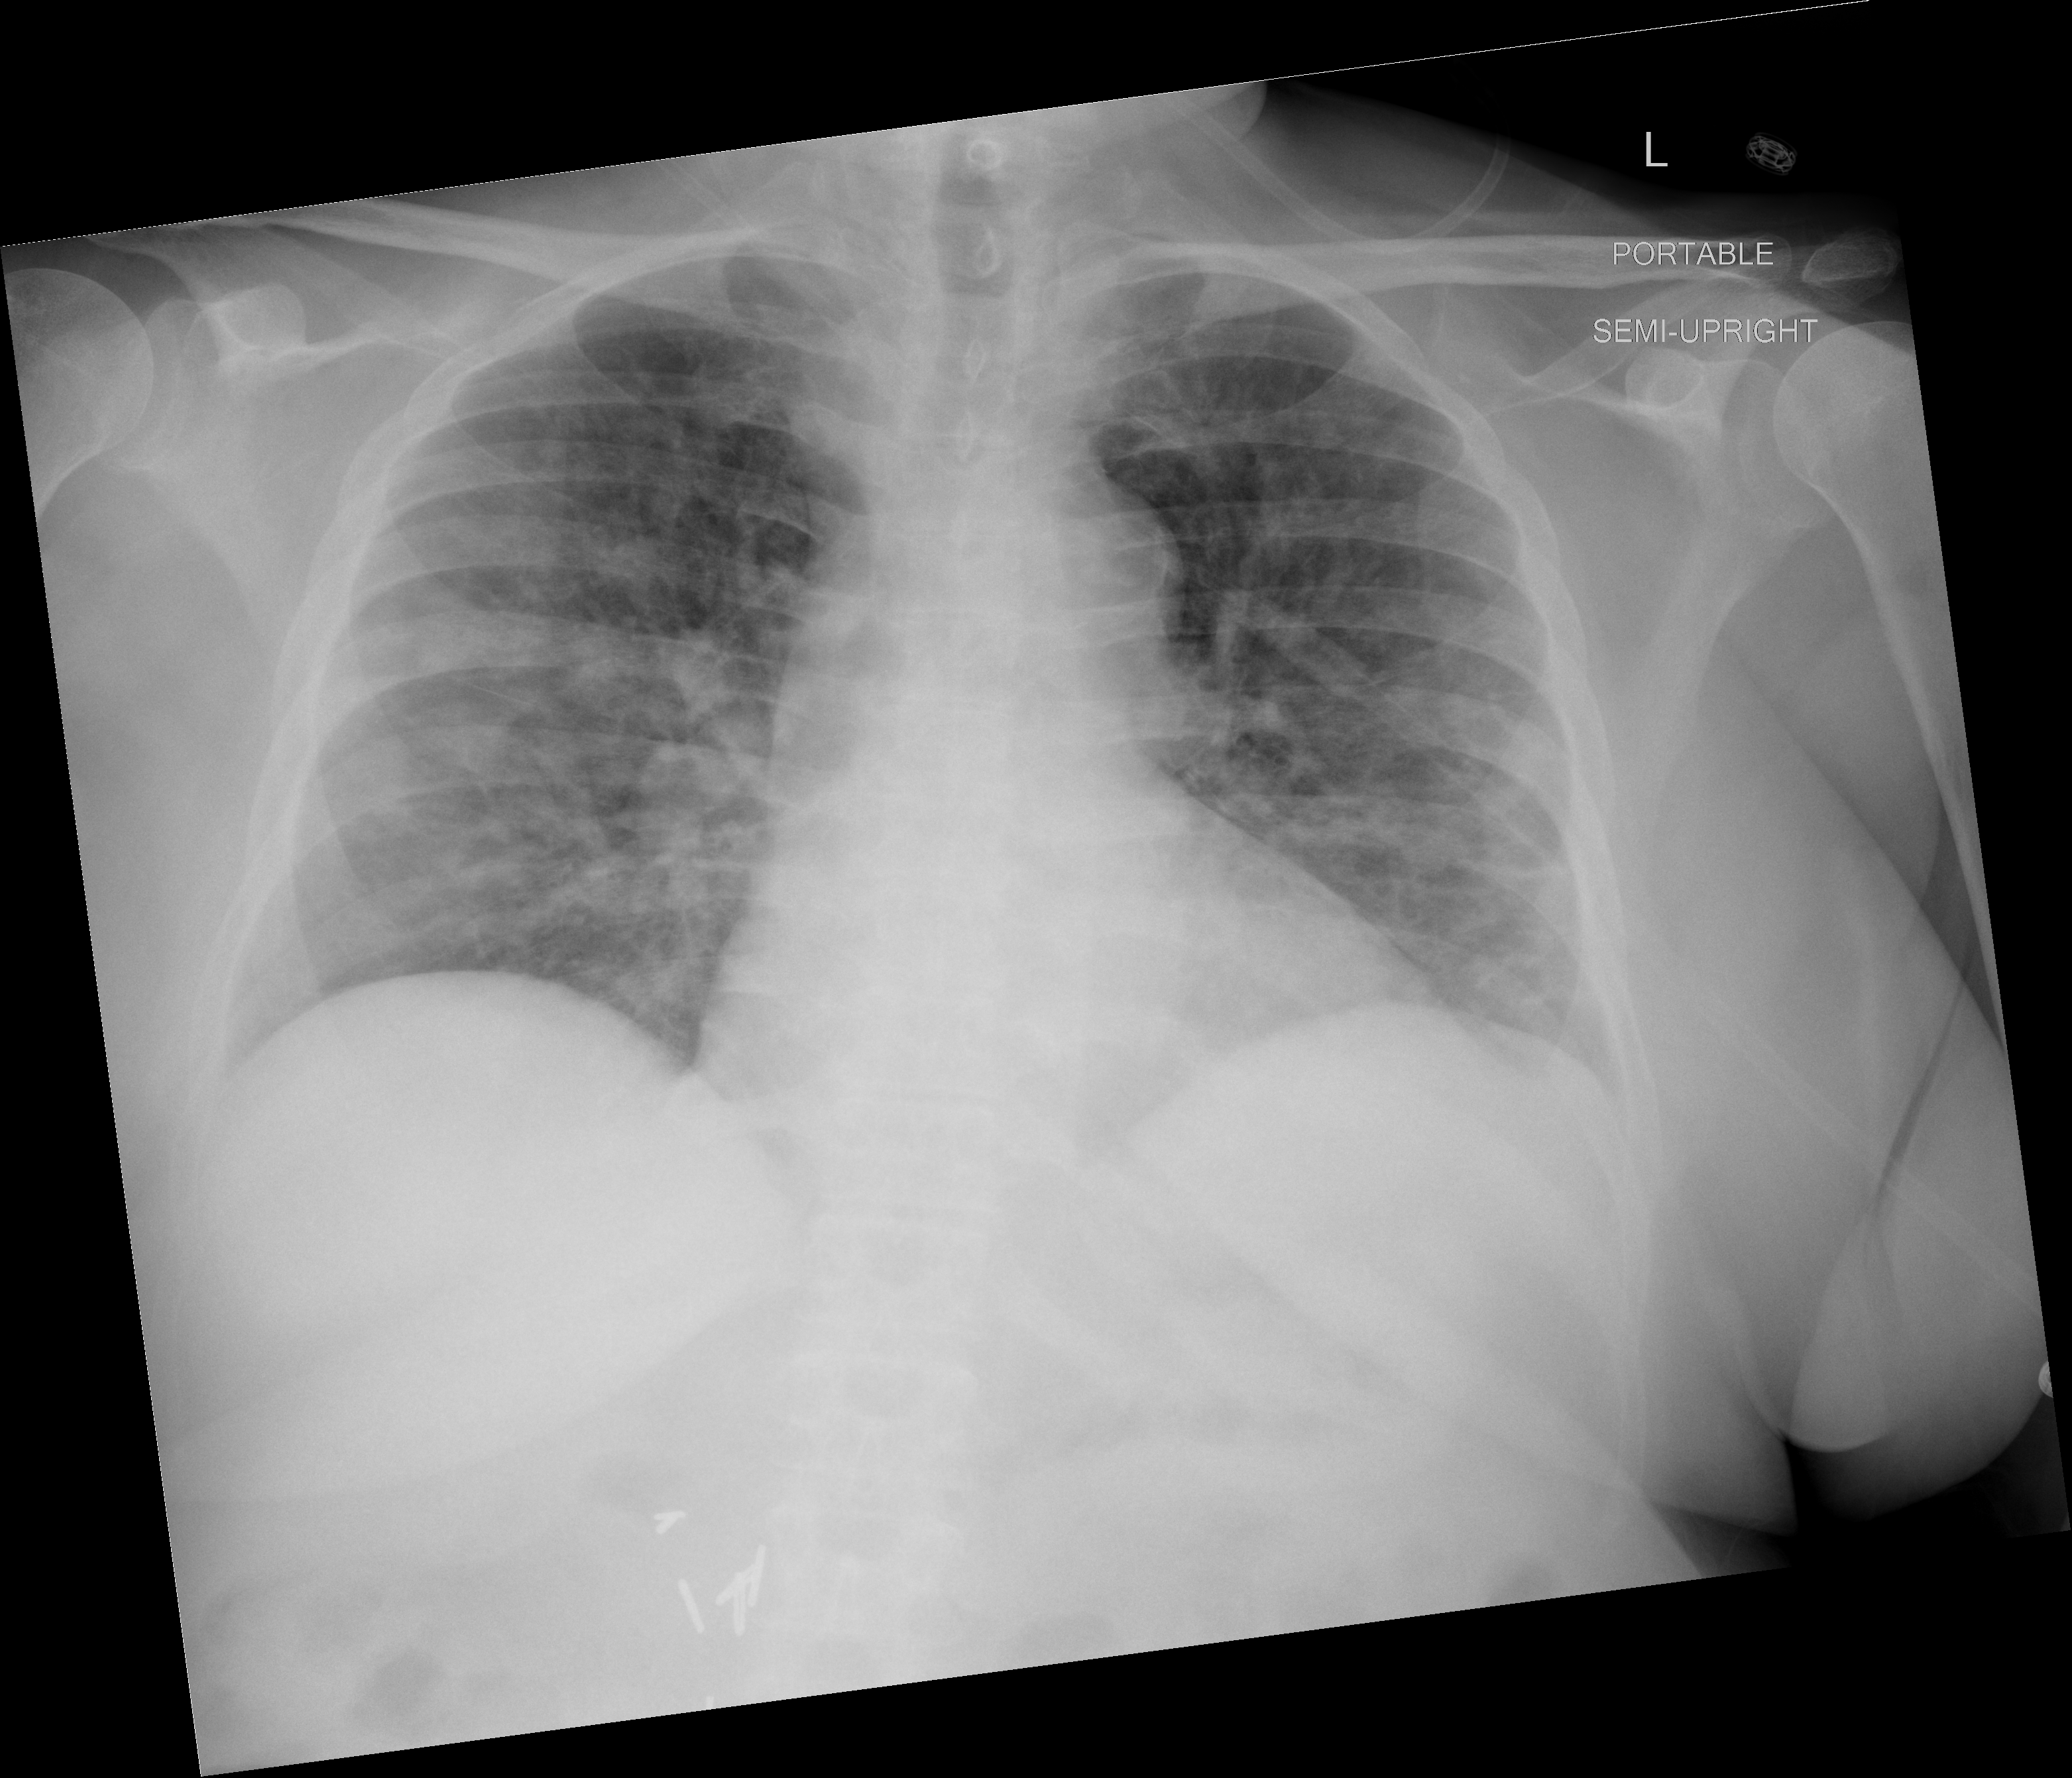
Chest X-ray (portable), AP projection. Female patient, age 65 years; imaged 7 days after the COVID-19 diagnosis.
Key findings recorded by the radiologist: Increased diffuse haziness consistent with airspace disease.